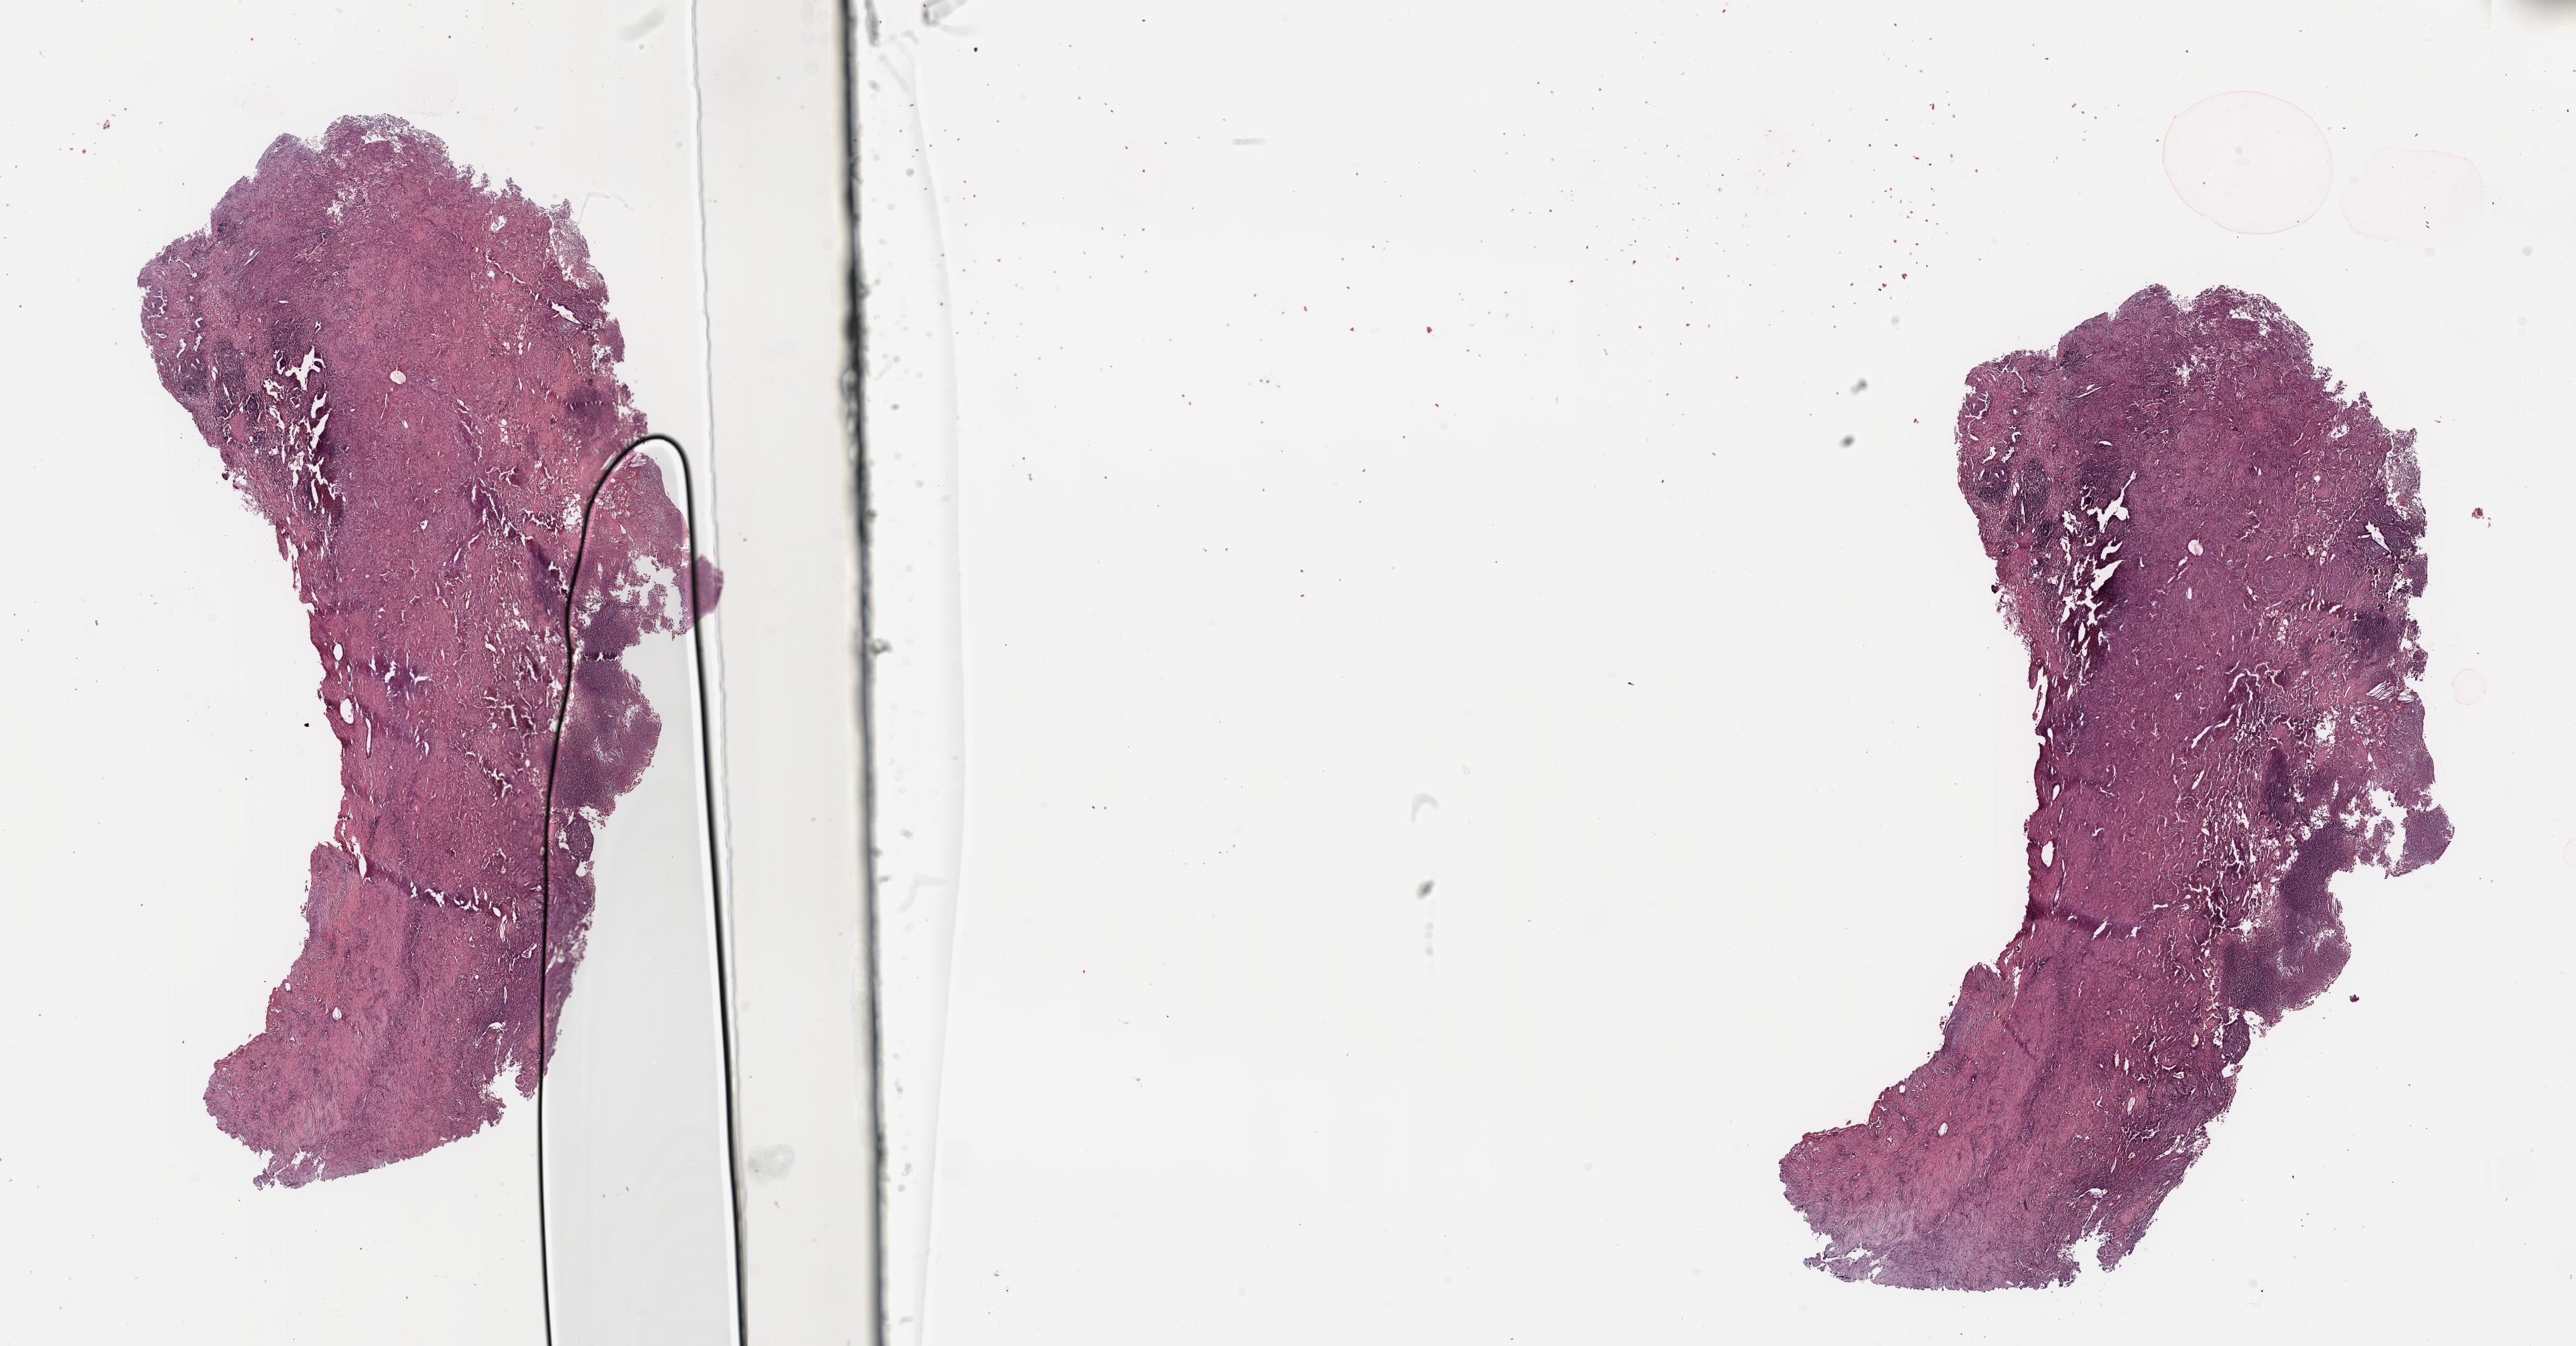
Whole-slide histology image, H&E, whole scanned area (about 30.5 x 16.0 mm, from a 20x scan) shown as a low-resolution overview, lung, tumour tissue. Patient: male, age 78 years. Histologic grade: G2 (moderately differentiated).
Histologic diagnosis: Squamous cell carcinoma, NOS. Primary tumour site (as recorded): left upper lobe. AJCC pathologic stage: IIA.